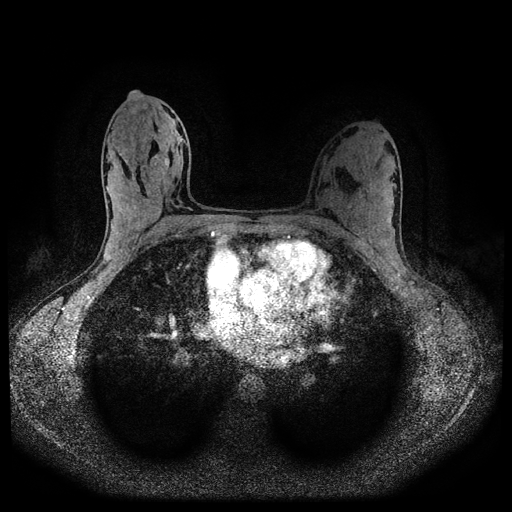
Breast MRI (dynamic contrast-enhanced, multi-phase), one axial slice; position 59 of 116 along the scan axis; dynamic contrast-enhanced series, time point 2 of 5 at this slice position (early post-contrast); 1.5 T; TE 2.7 ms, TR 5.4 ms; 2 mm slice thickness; 512 × 512 image matrix, field of view 330 × 330 mm. Patient: female, 32 years.
Annotated regions visible in this slice (semi-automatic segmentation, software-assisted and operator-edited):
- breast lesion (labelled benign in the annotation): bounding box <111,159,120,180> (left, top, right, bottom; pixels)